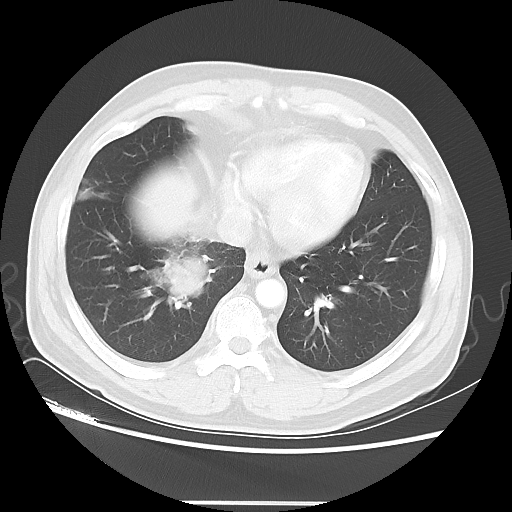
Chest CT, one axial slice. Slice 13 of 48 in the series (ordered by position). Reconstruction kernel LUNG. Lung window (W 1500 / L -600 HU). 5 mm slice thickness. 512 × 512 image matrix, field of view 390 × 390 mm. Patient: male, 53 years. Case-level facts recorded for this patient, not image findings: clinical TNM (as recorded): T2 N3 M0.
Structures marked on this image (bounding box drawn by a radiologist):
- lung tumour (recorded histology: small cell carcinoma): bounding box <158,252,214,311> (left, top, right, bottom; pixels)